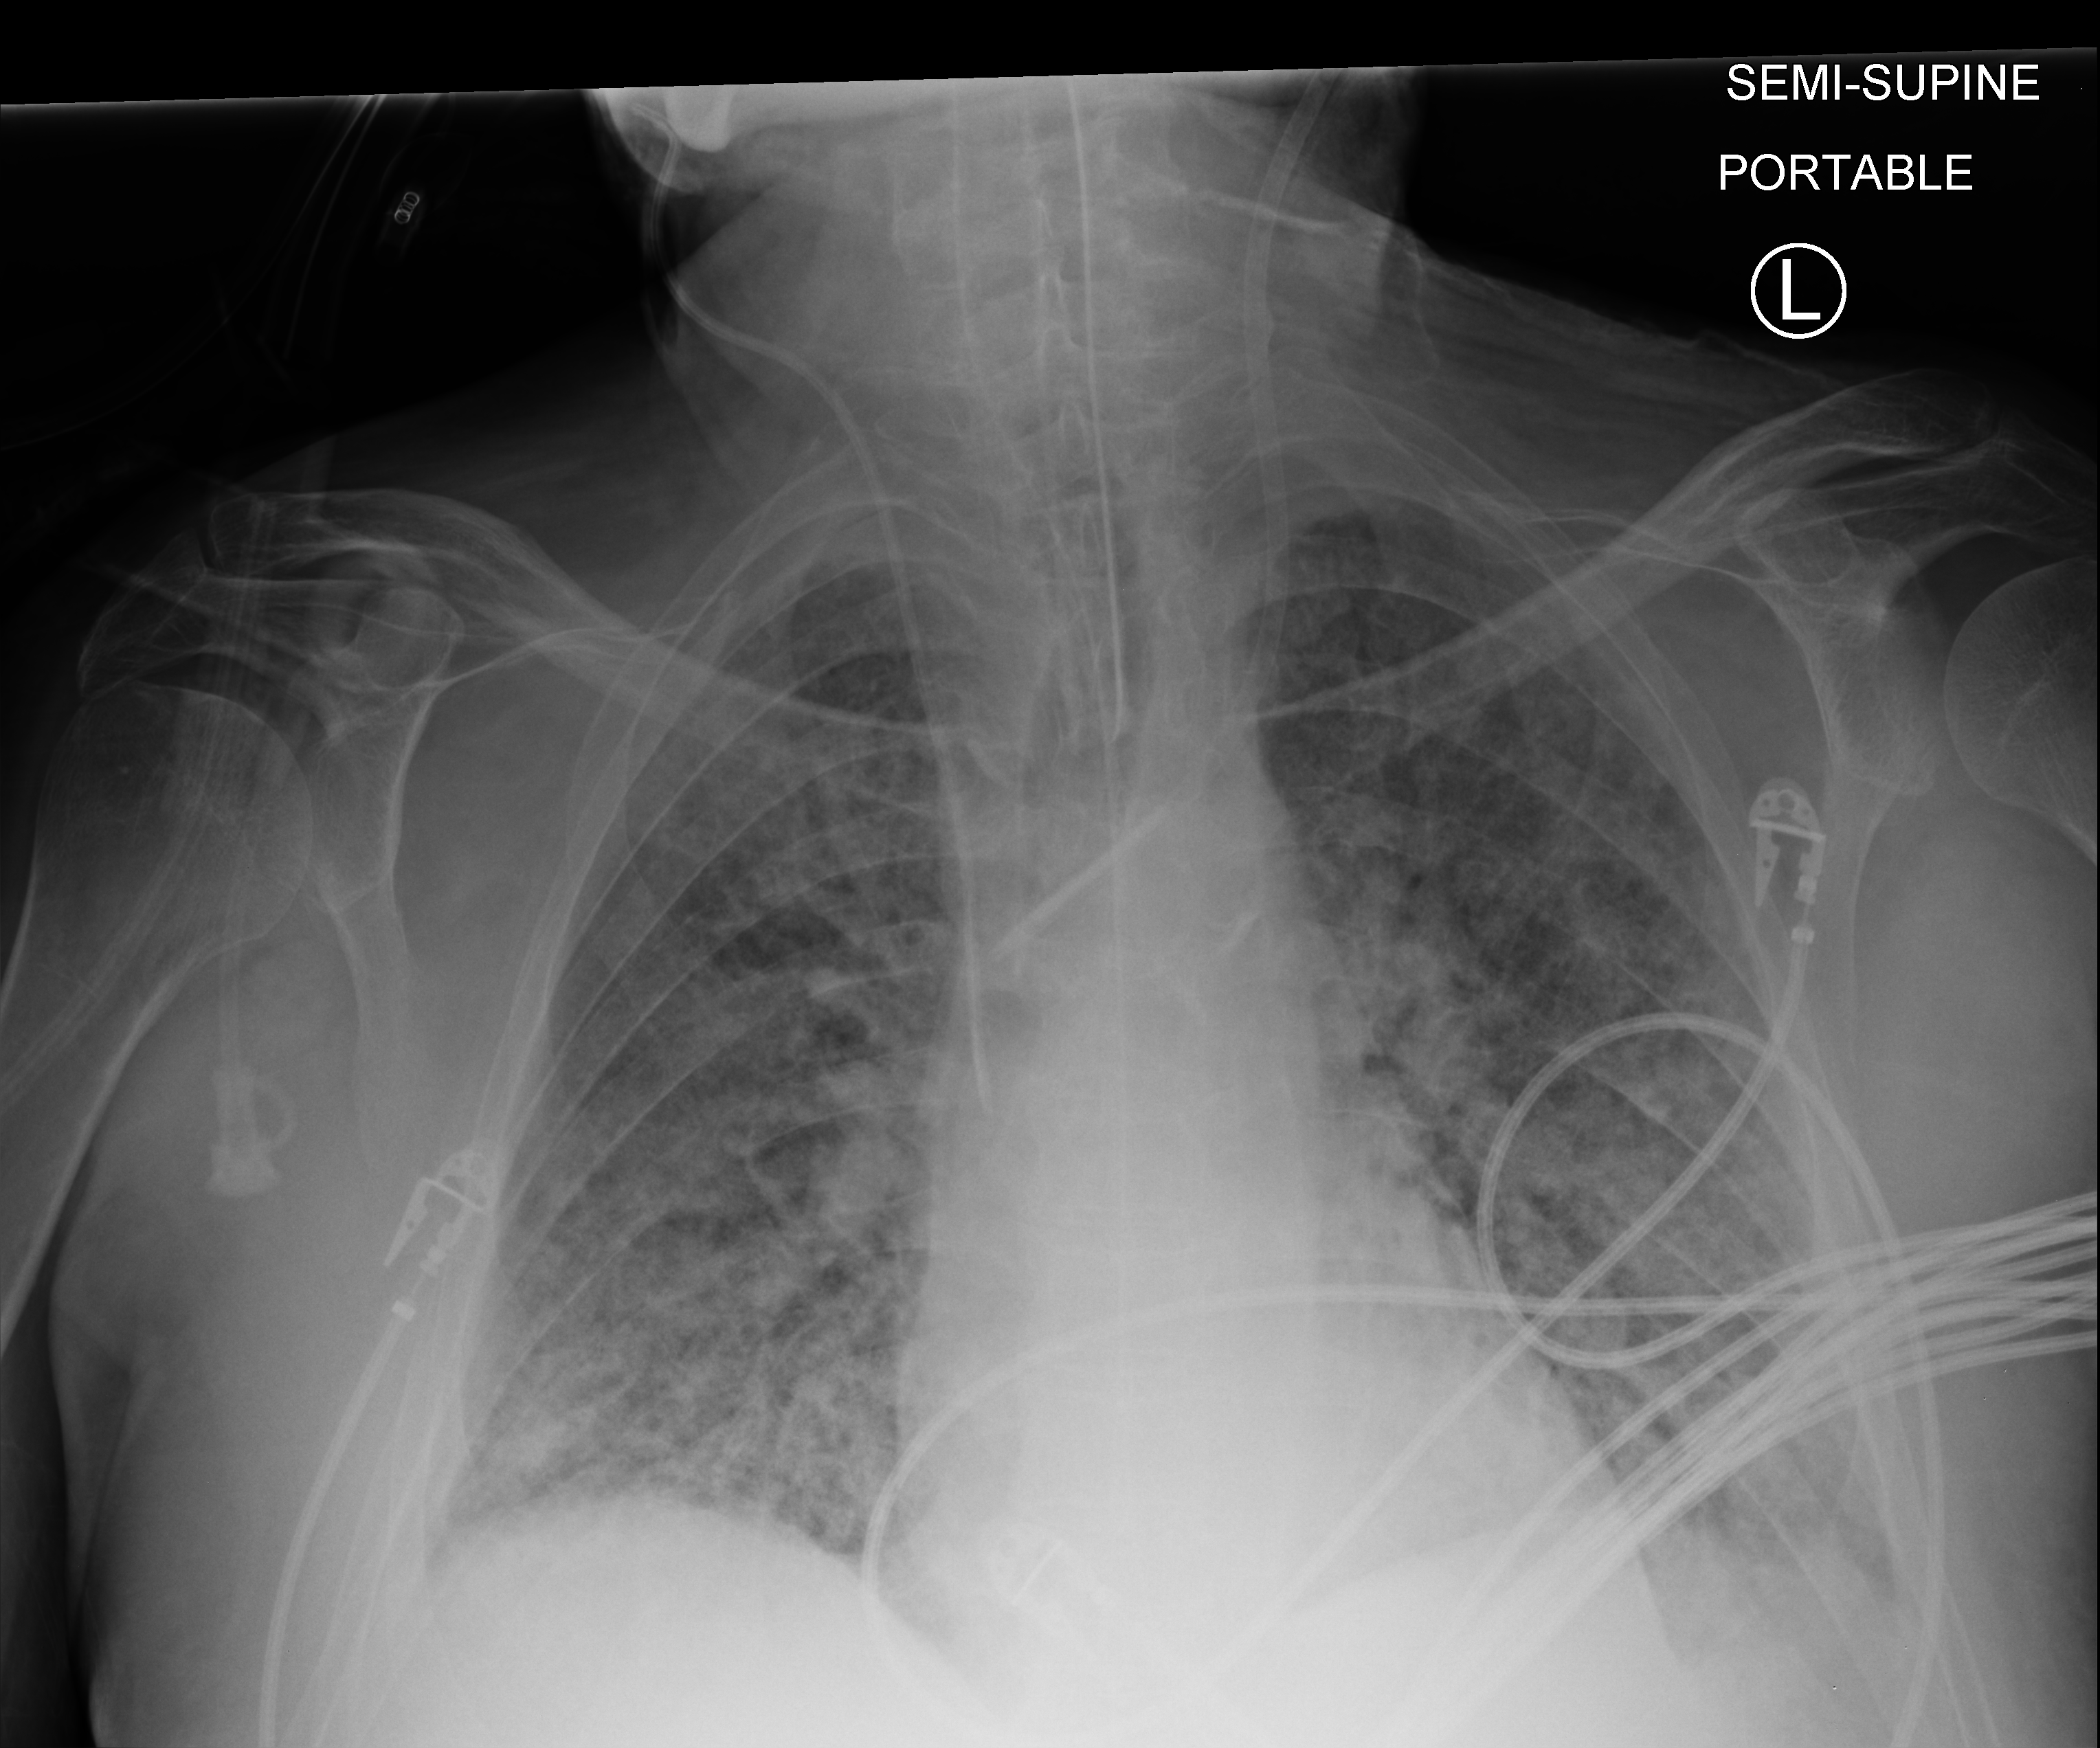
Bedside chest radiograph (computed radiography). Male patient hospitalised with COVID-19, age 60–74 years.
Hospital-stay facts (about this admission, not read from this image; timing relative to this image not recorded): admitted to intensive care during this hospital stay: yes; hypertension (admission record): no; chronic kidney disease (admission record): no.